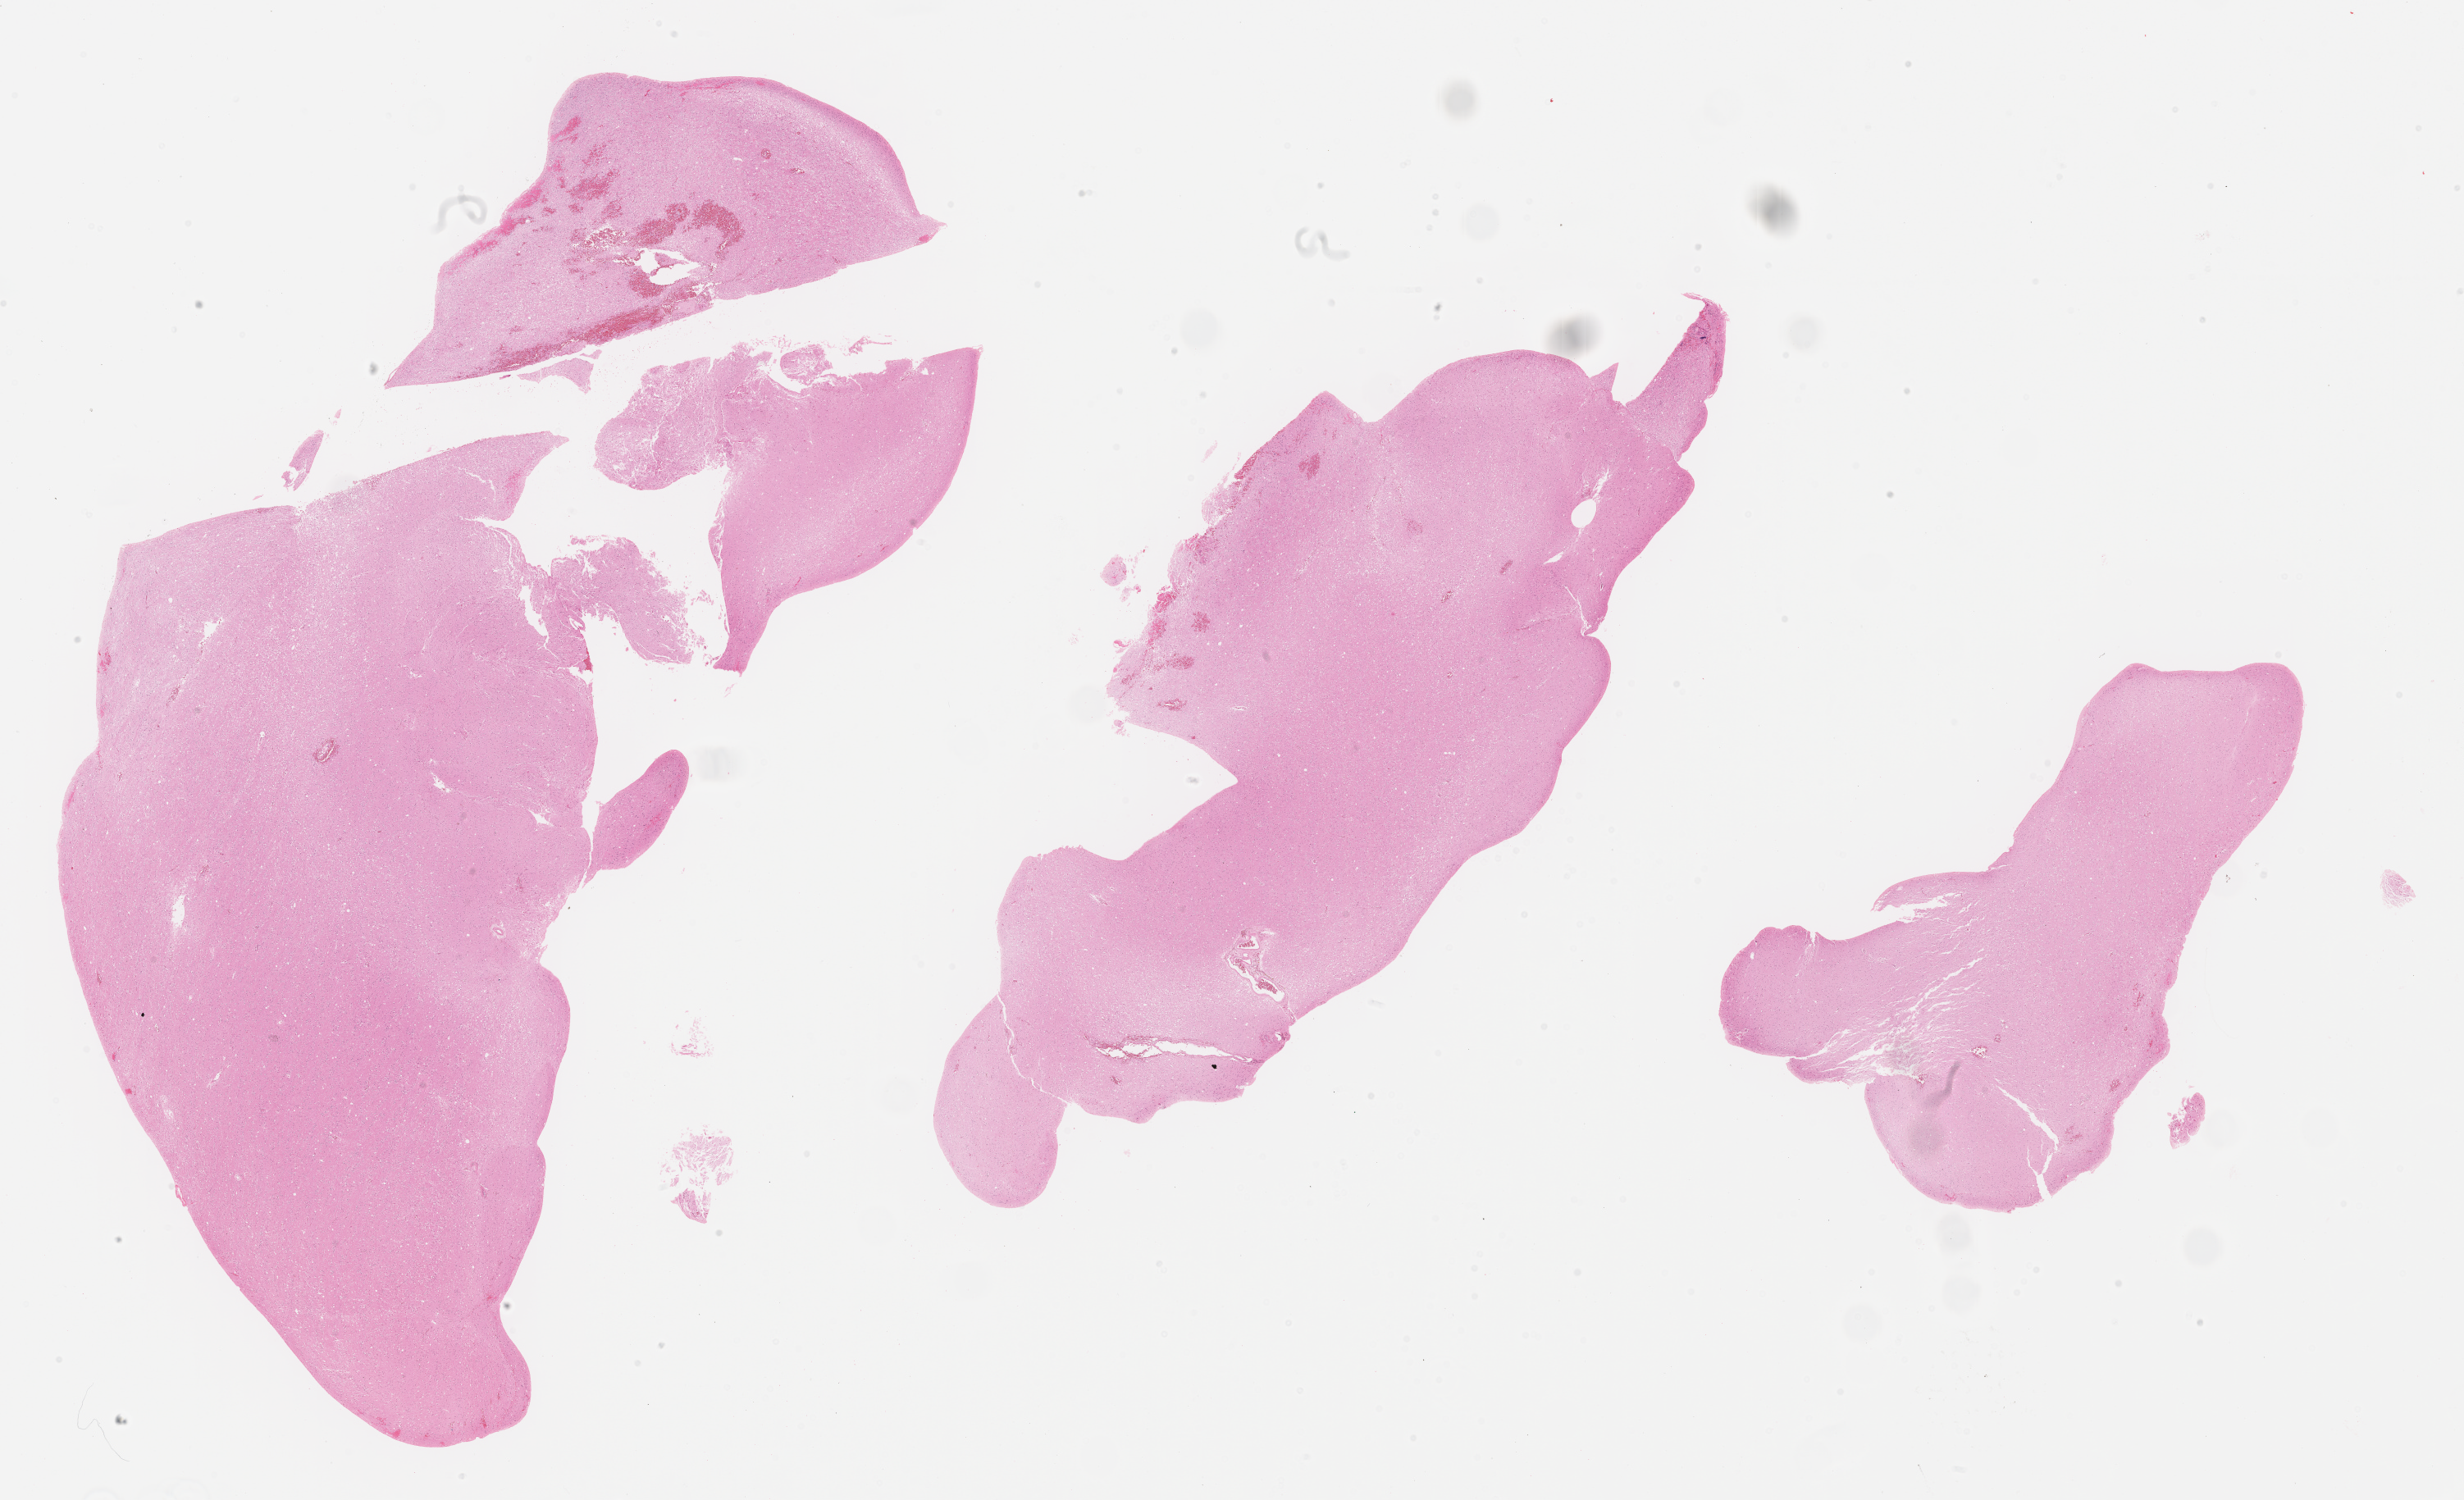
Digitized H&E tissue section (whole slide) — shown as a low-resolution overview of the whole scanned area (about 24.2 x 14.7 mm). Formalin-fixed paraffin-embedded (FFPE) diagnostic section. Primary tumour sample from the brain. Male, age 40 years at initial diagnosis. Histologic grade: G2 (moderately differentiated).
Laterality: right. Histologic diagnosis: Oligodendroglioma, NOS (cerebrum).